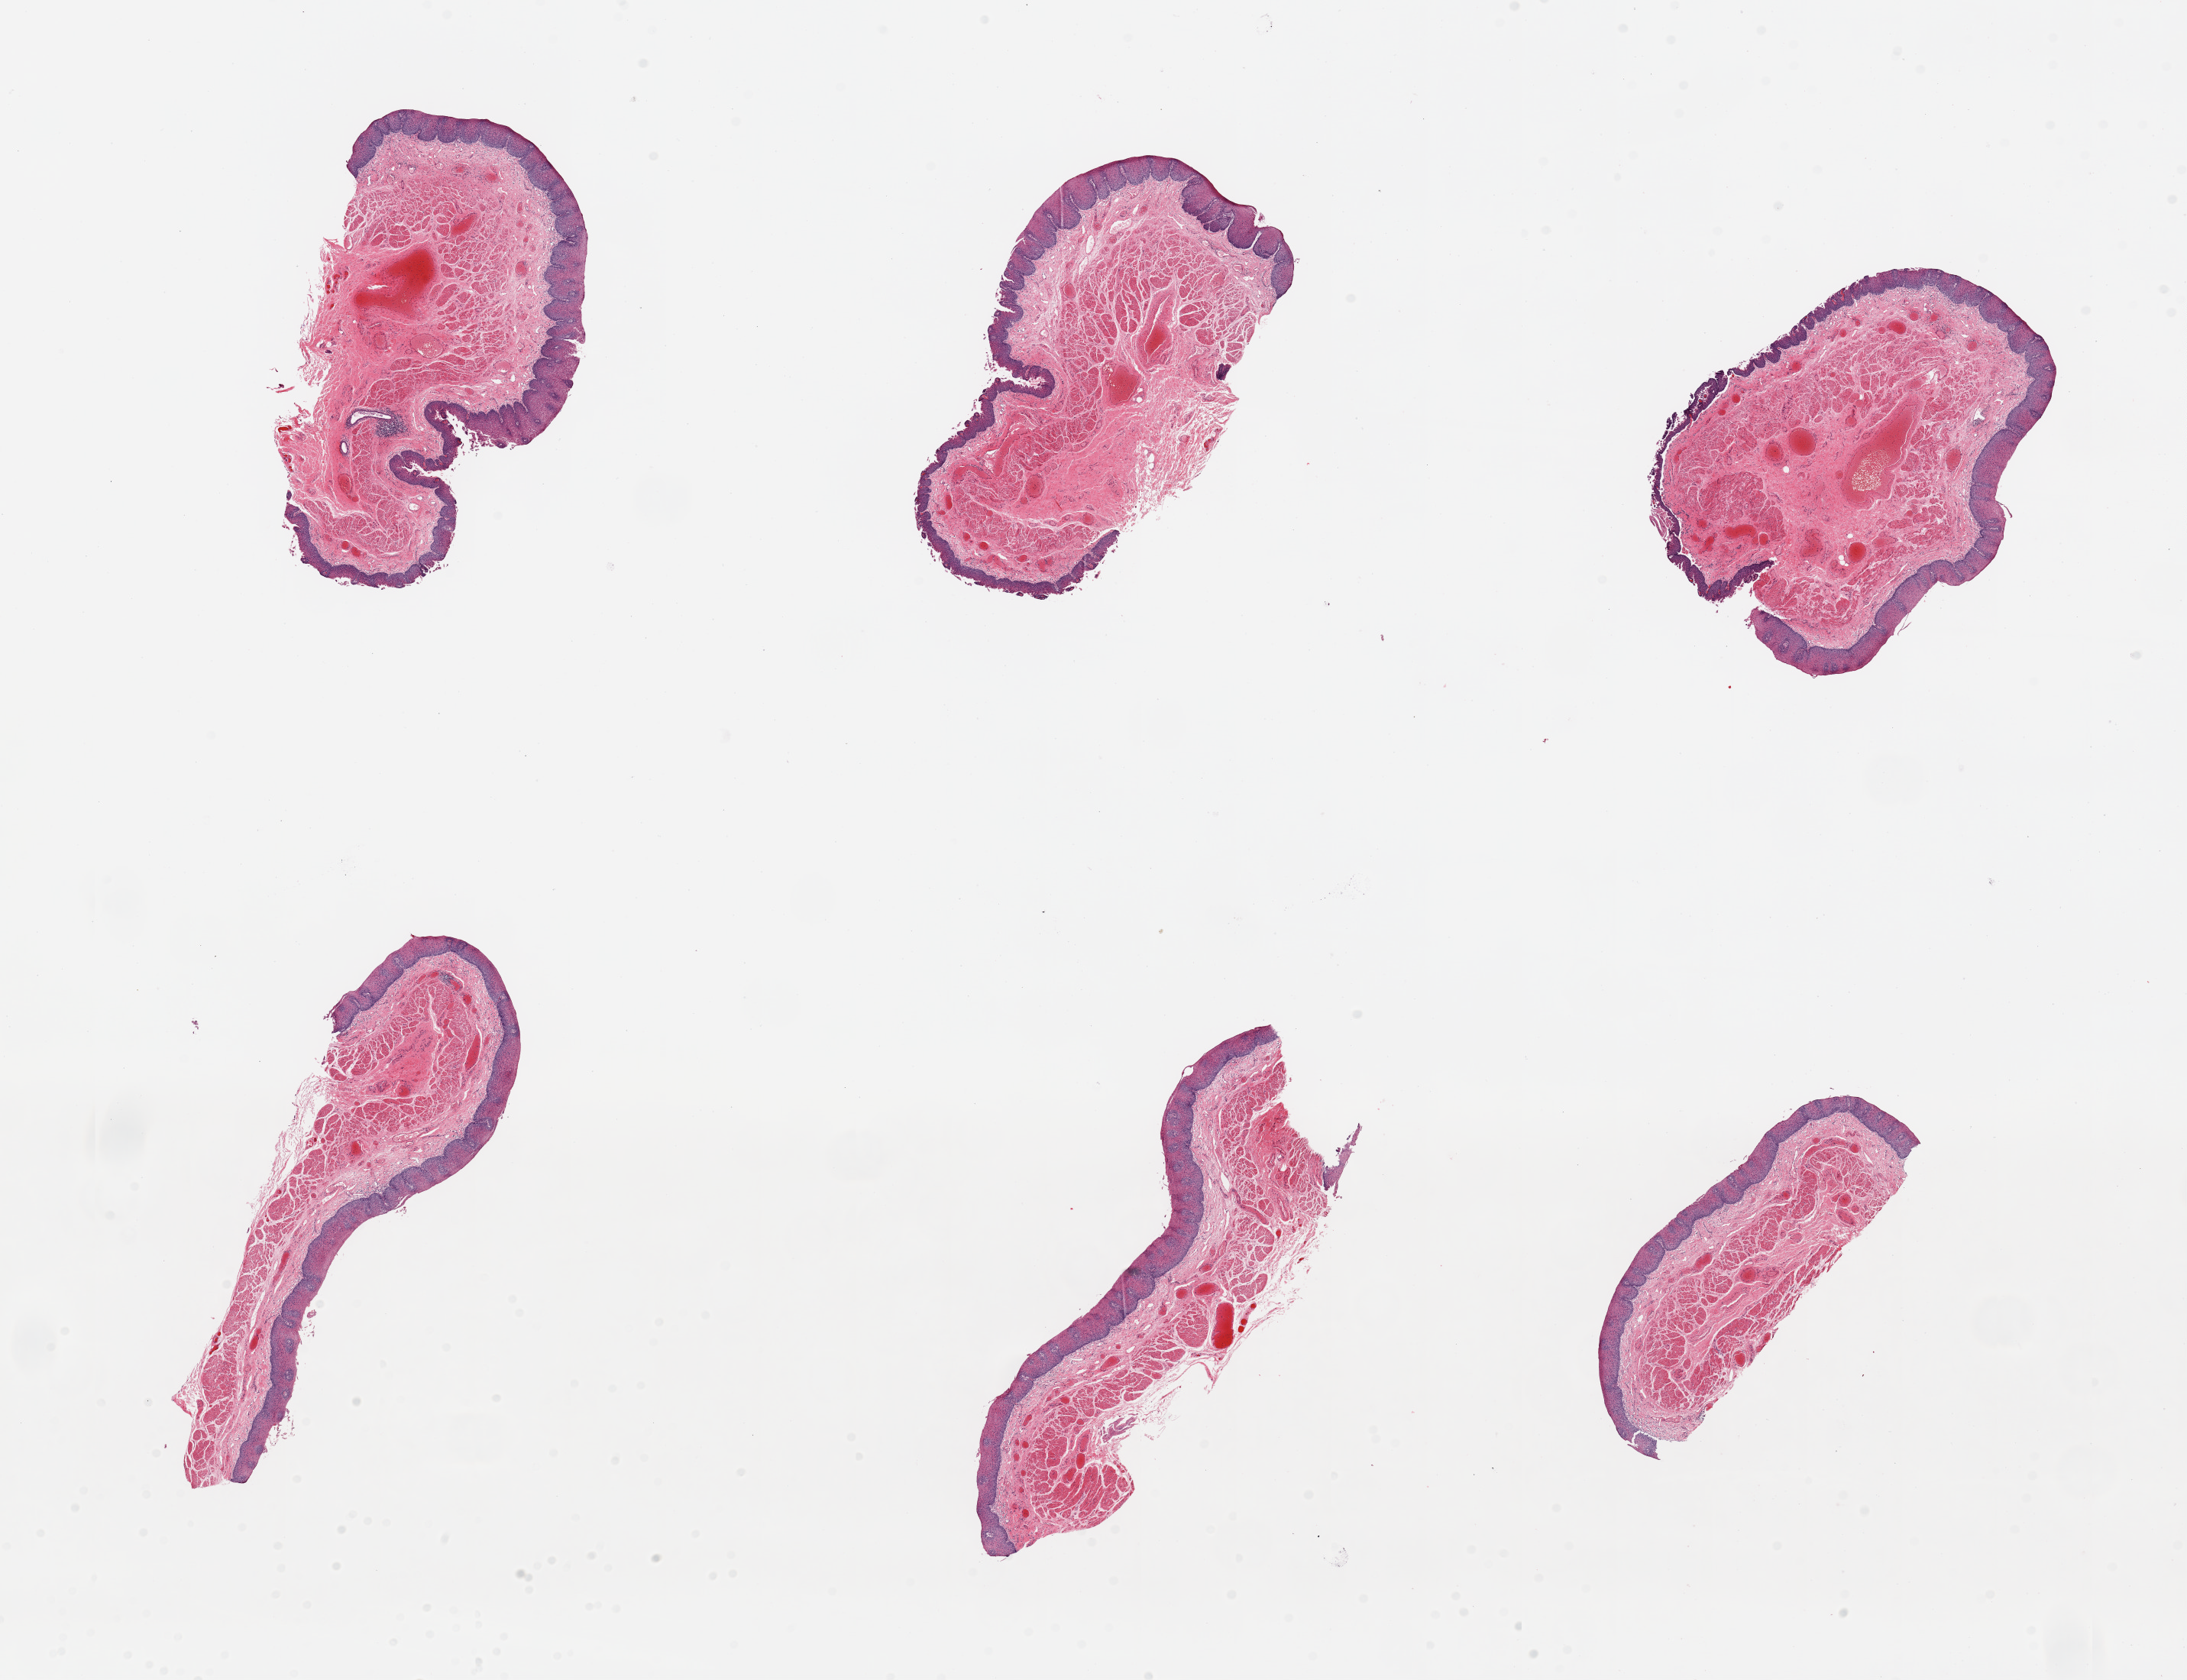
Whole-slide image, haematoxylin and eosin stain, a low-resolution overview of the entire scanned area, about 22.6 x 17.4 mm, PAXgene-fixed paraffin-embedded (PFPE) section, sampled site (target tissue): esophageal mucous membrane, donor tissue sample.
Review note (as recorded): 6 pieces; focal desquamation; 3 pieces are moderately congested.